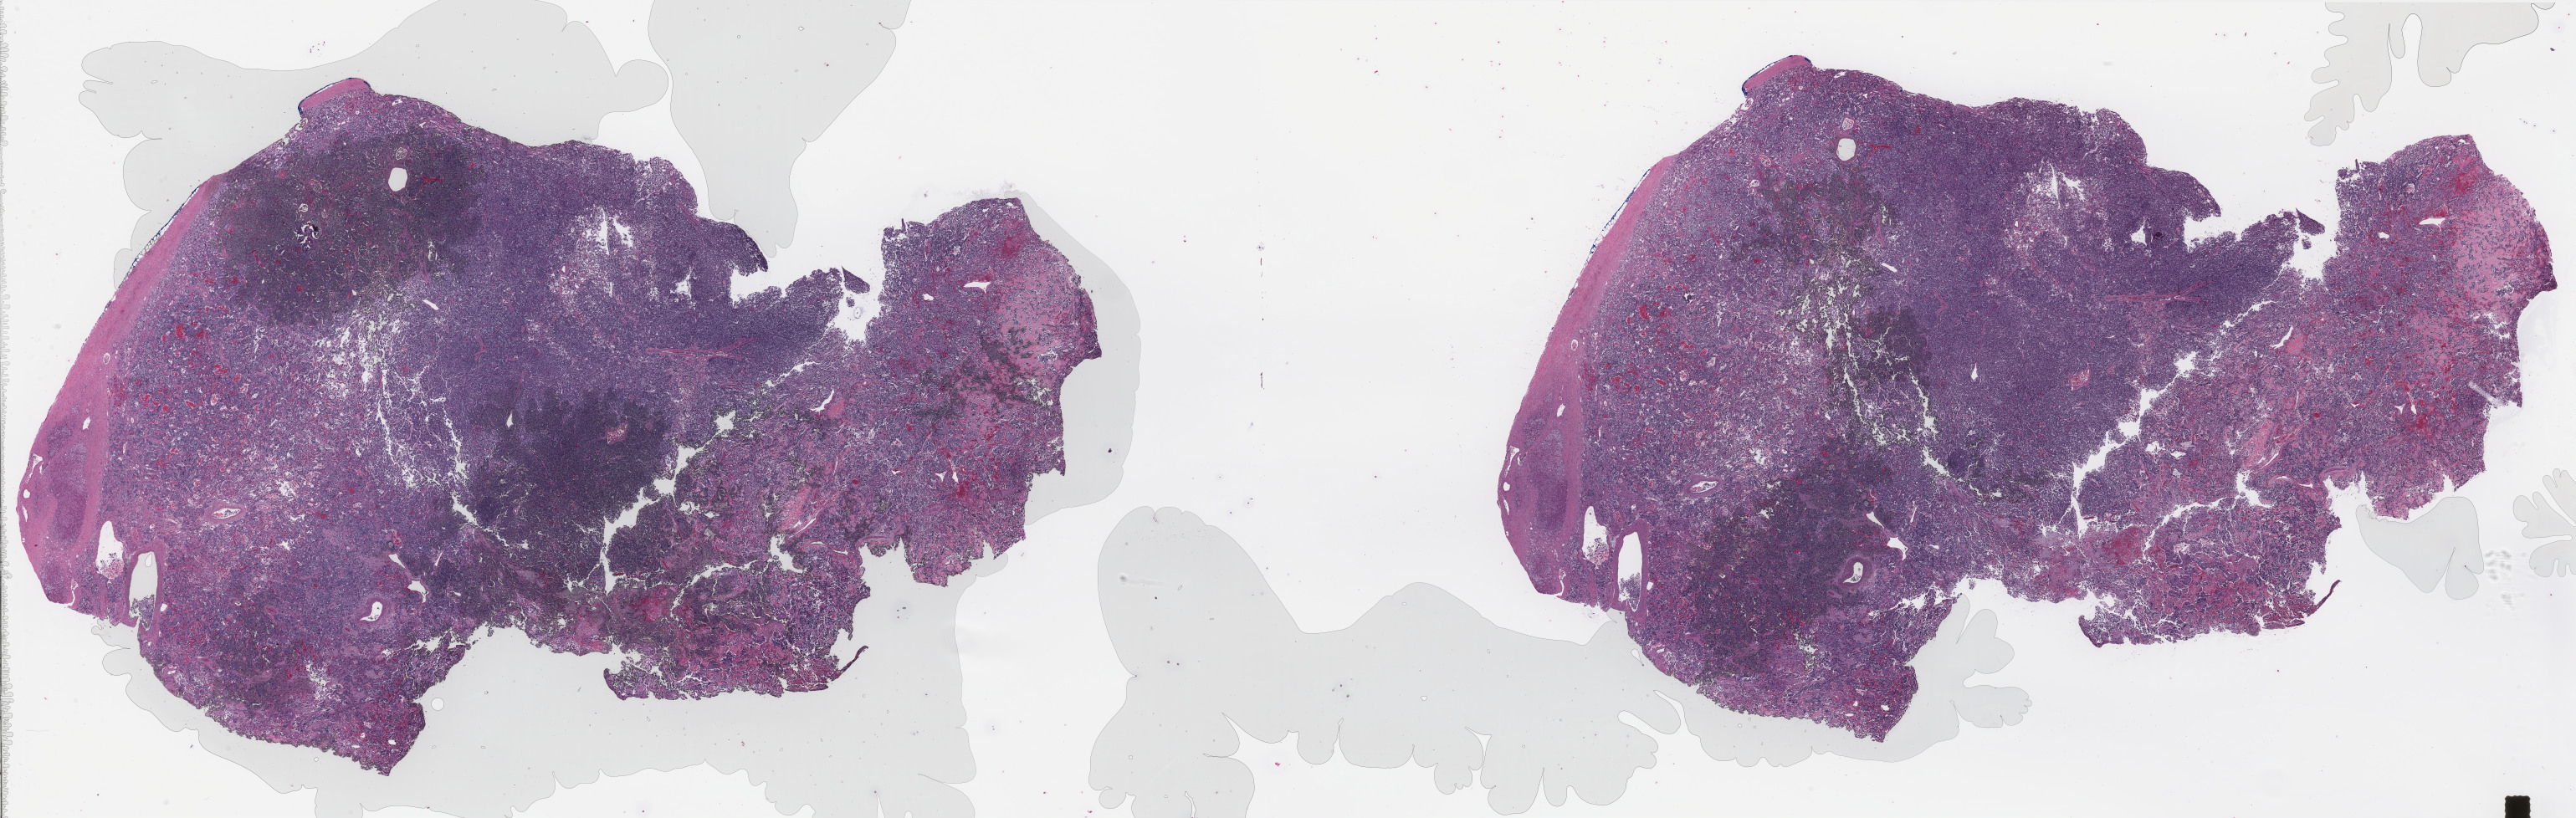
Whole-slide histology image, H&E-stained — low-resolution overview of the scanned area, about 48.7 x 15.5 mm. Formalin-fixed paraffin-embedded (FFPE) diagnostic section. Adrenal gland, primary tumour sample. Female patient; age at initial diagnosis 57 years.
Histologic diagnosis: Pheochromocytoma, malignant.